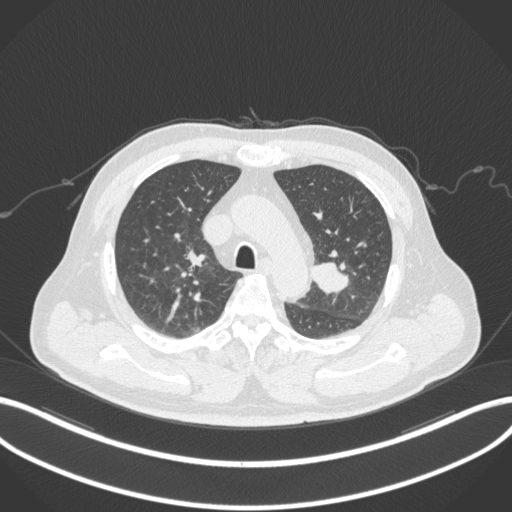
Chest CT, one axial slice; position 217 of 286 along the scan axis; reconstruction kernel B31f; 120 kVp; lung window (W 1500 / L -600 HU); 1 mm slice thickness; 512 × 512 image matrix, field of view 400 × 400 mm. Male patient, age 67 years. From the clinical record (not read from this slice): clinical TNM (as recorded): T2a N1 M0; histopathological grade: G3.
Outlined on this slice (rectangle marked by the reading radiologist):
- lung tumour (recorded histology: adenocarcinoma): bounding box <307,257,352,298> (left, top, right, bottom; pixels)